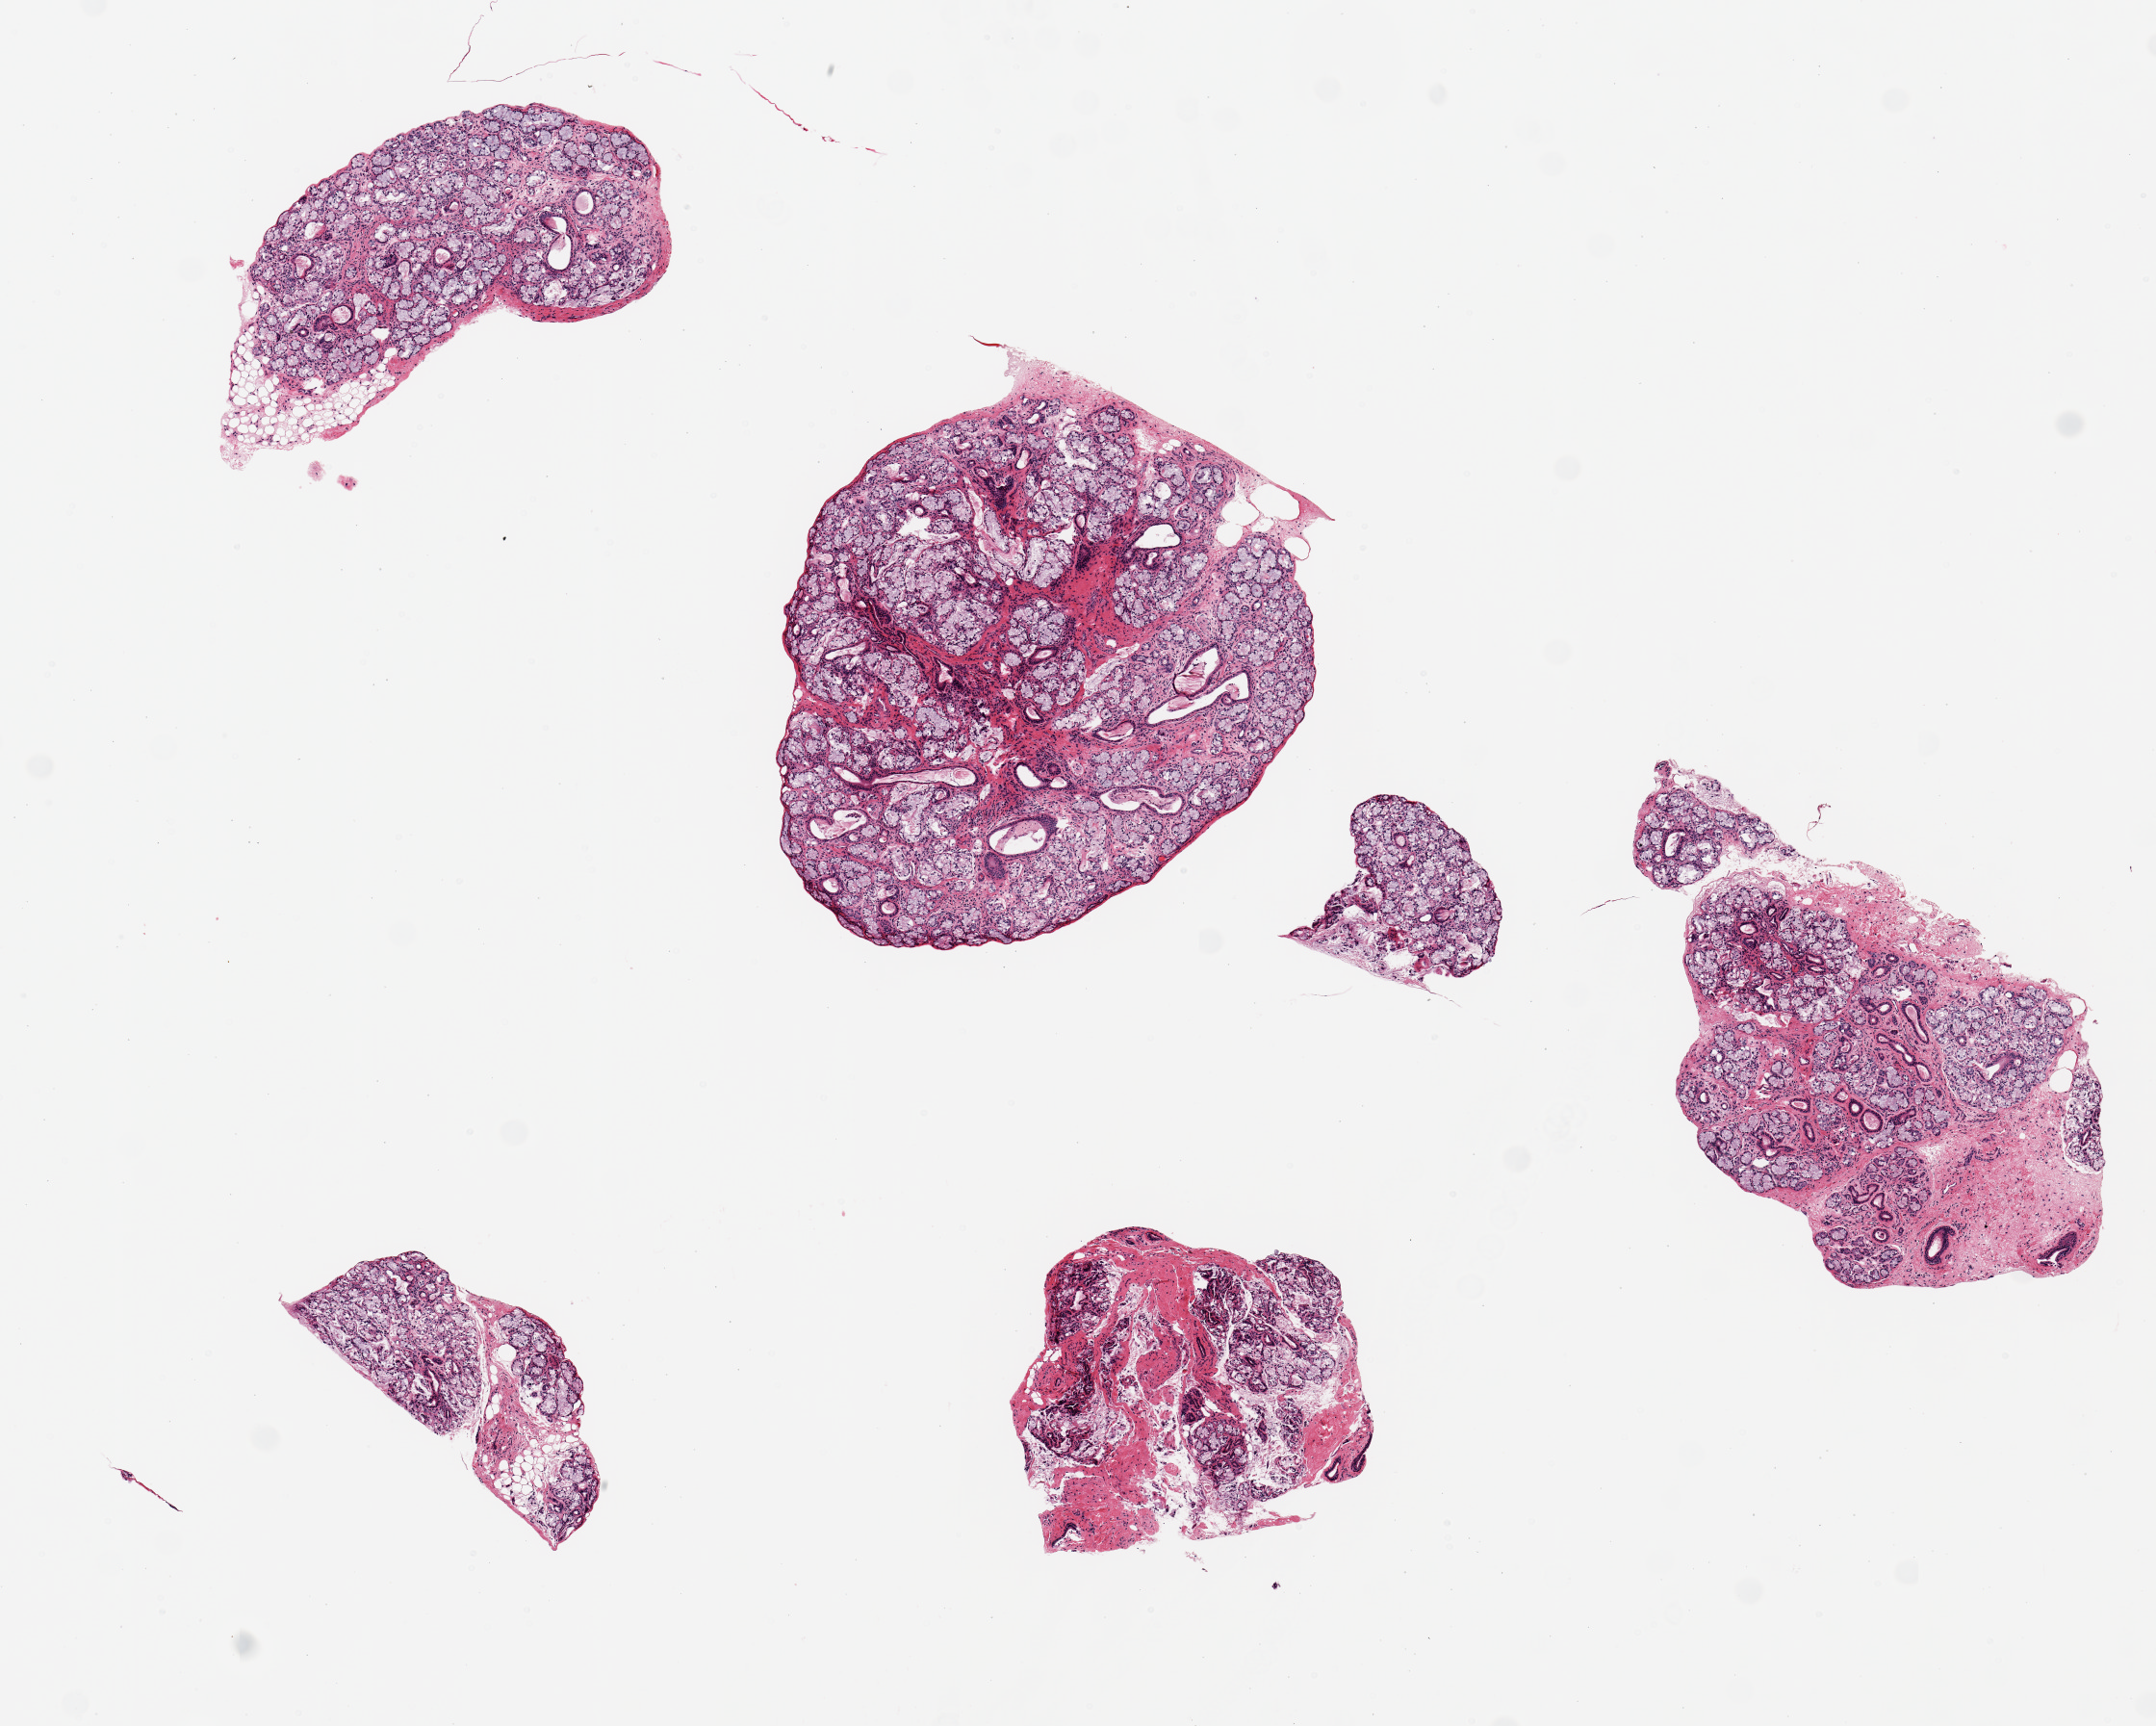
Whole-slide image, haematoxylin and eosin stain, a low-resolution overview of the entire scanned area, about 8.9 x 7.1 mm (from a 20x scan); PAXgene-fixed paraffin-embedded (PFPE) section; section of minor salivary gland (target tissue); donor tissue sample.
Reviewer comment on this tissue sample: 6 pieces, up to 2x2mm; very good well trimmed samples especially largest.